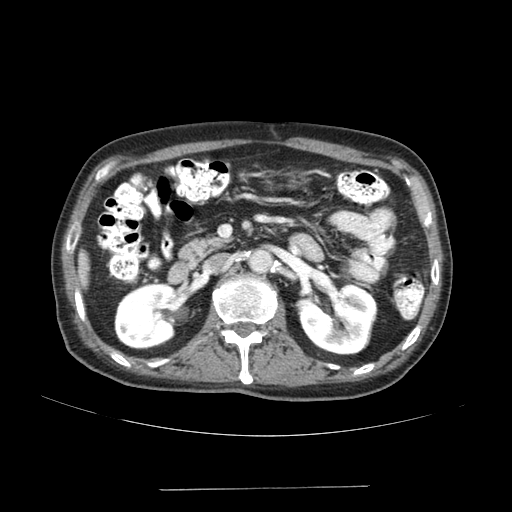
Contrast-enhanced abdominal CT (liver protocol), one axial slice; position 54 of 192 along the scan axis; soft-tissue window (W 400 / L 40 HU); 2.5 mm slice thickness; 512 × 512 image matrix. Case-level facts recorded for this patient, not image findings: diagnosis: hepatocellular carcinoma (patient treated with transarterial chemoembolisation; whether this scan precedes or follows treatment is not stated here); TNM stage (as recorded): Stage-IVA; Child-Pugh class: A; tumour differentiation: poorly differentiated.
Annotated regions visible in this slice (semi-automatically segmented with operator editing):
- liver parenchyma outside the tumour (the mass and vessels are separate outlines, so this box may not span the whole liver): box from (x=78, y=250) to (x=88, y=286) px